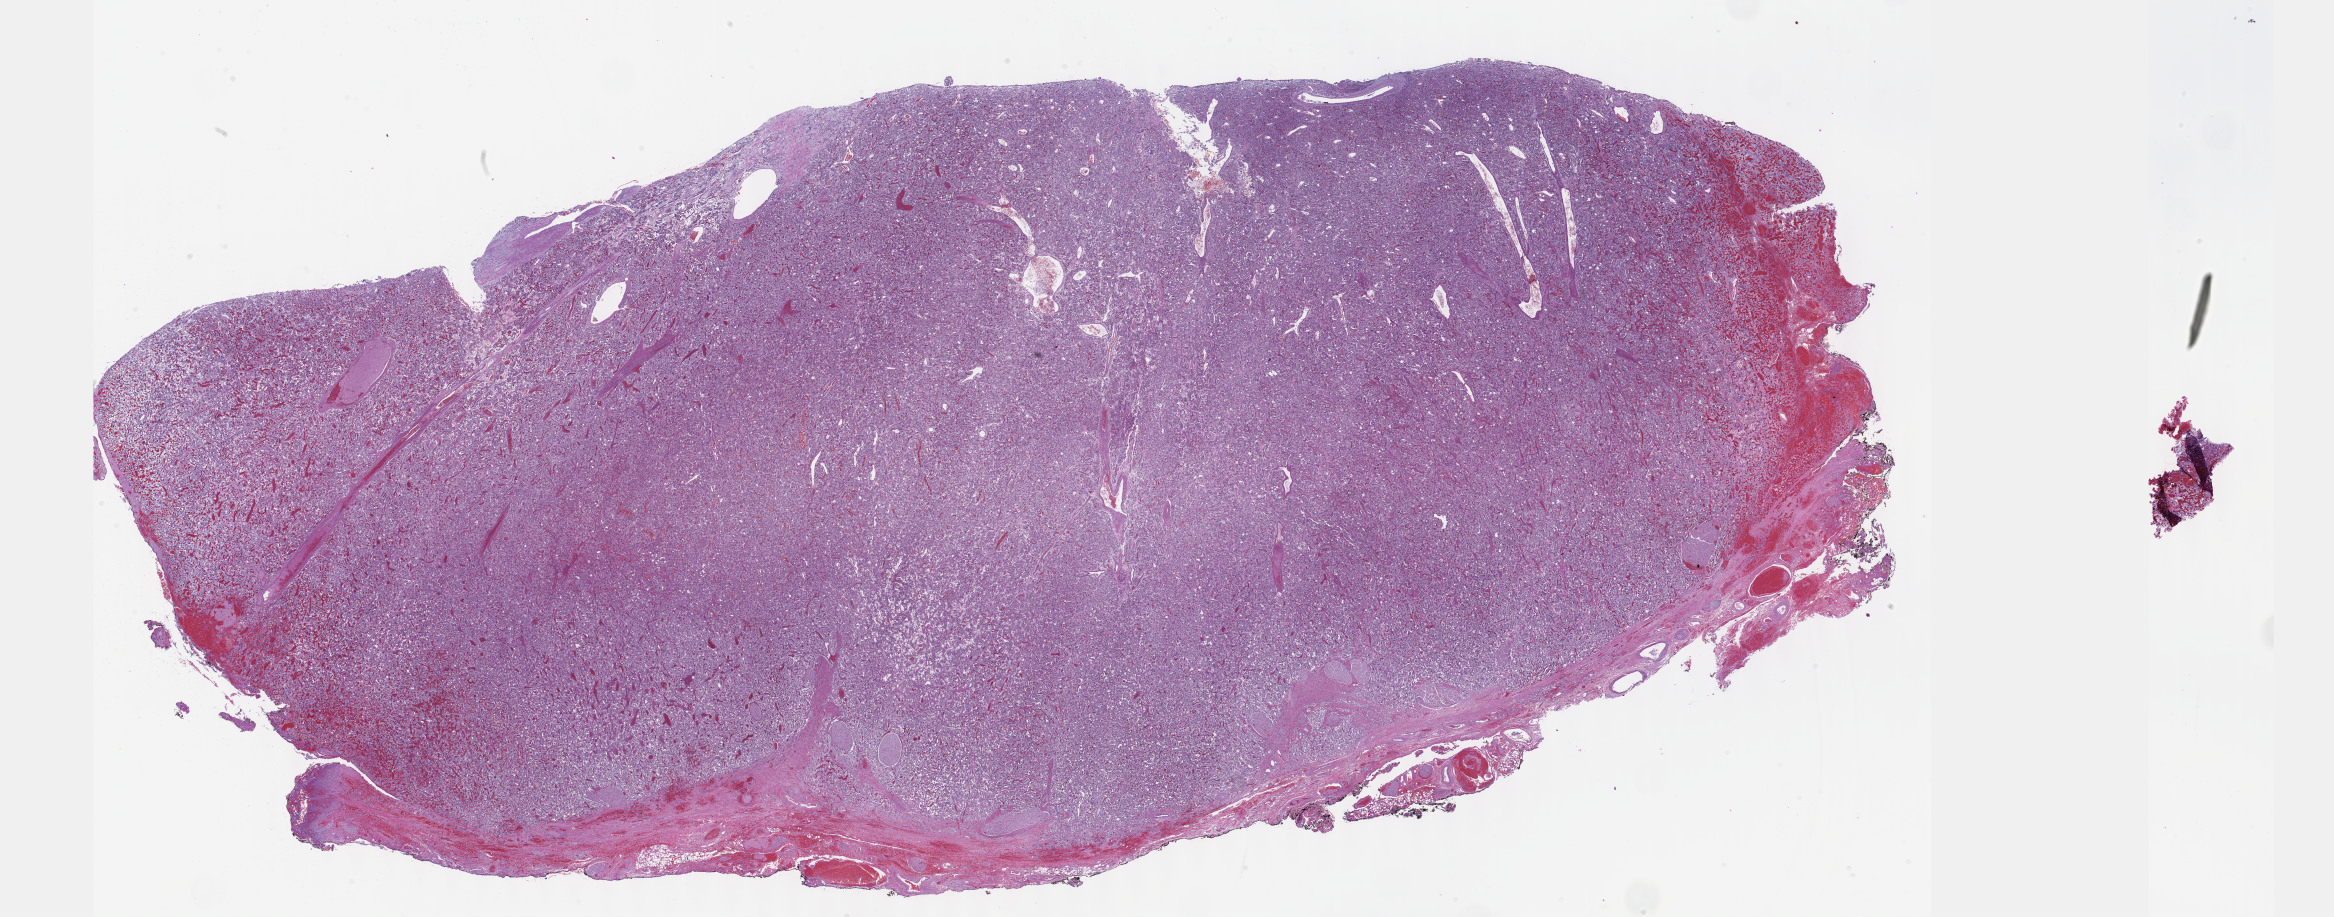
Digitized H&E tissue section (whole slide) — whole scanned area (about 37.7 x 14.8 mm, from a 40x scan) shown as a low-resolution overview, formalin-fixed paraffin-embedded (FFPE) diagnostic section, primary tumour sample from the retroperitoneum and peritoneum. Male, age 24 years at initial diagnosis.
Histologic diagnosis: Extra-adrenal paraganglioma, NOS.